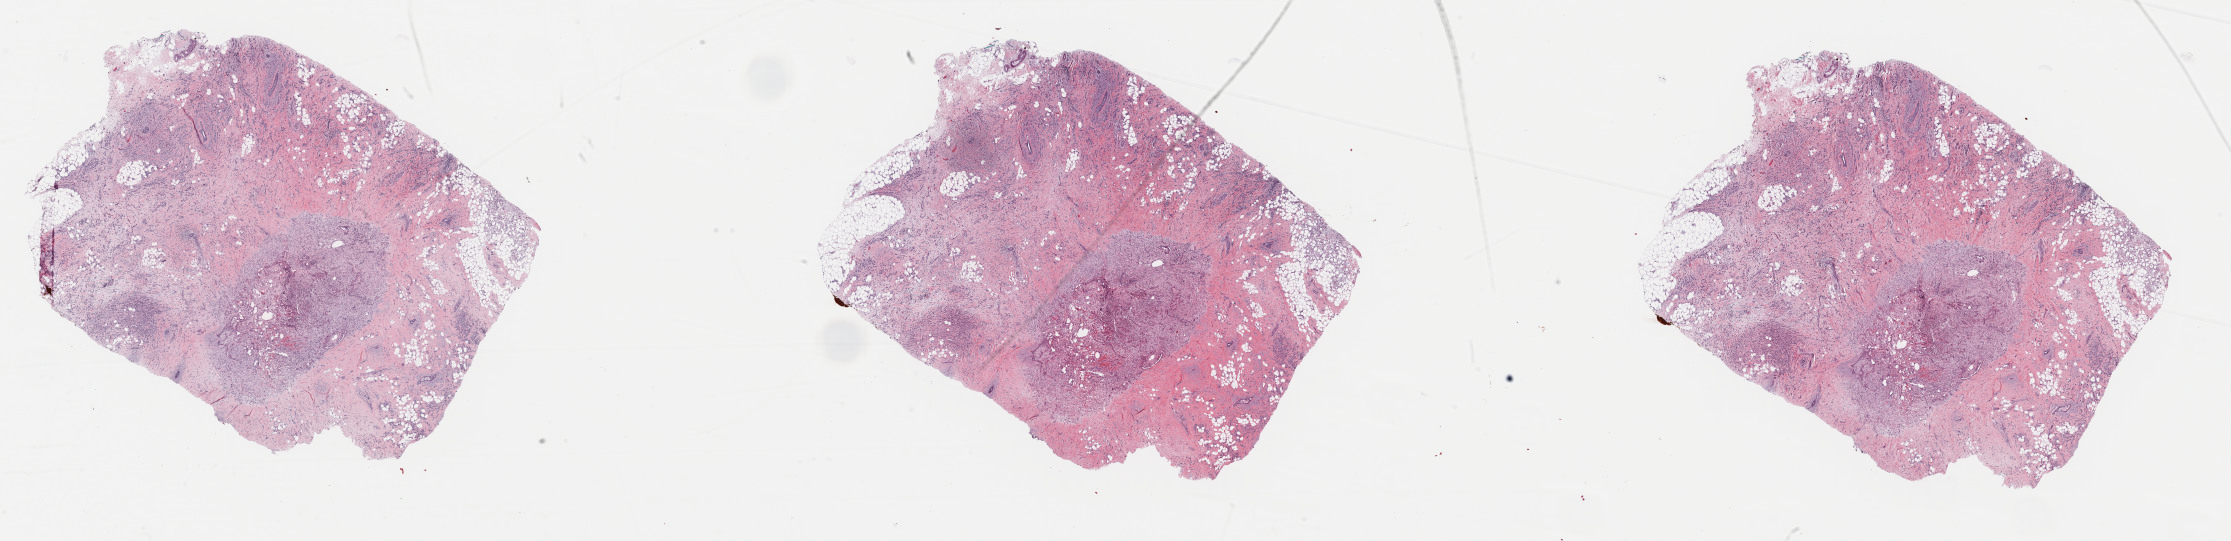
Digitized H&E-stained tissue section (whole slide), whole scanned area (about 35.2 x 8.5 mm, slide scanned at 40x) shown as a low-resolution overview; FFPE section; breast, primary tumour sample. Patient: female, age at initial diagnosis 78 years.
AJCC pathologic stage: IIA. Lymph nodes positive (case pathology): 0 of 5 examined. Histologic diagnosis: Infiltrating duct and lobular carcinoma.